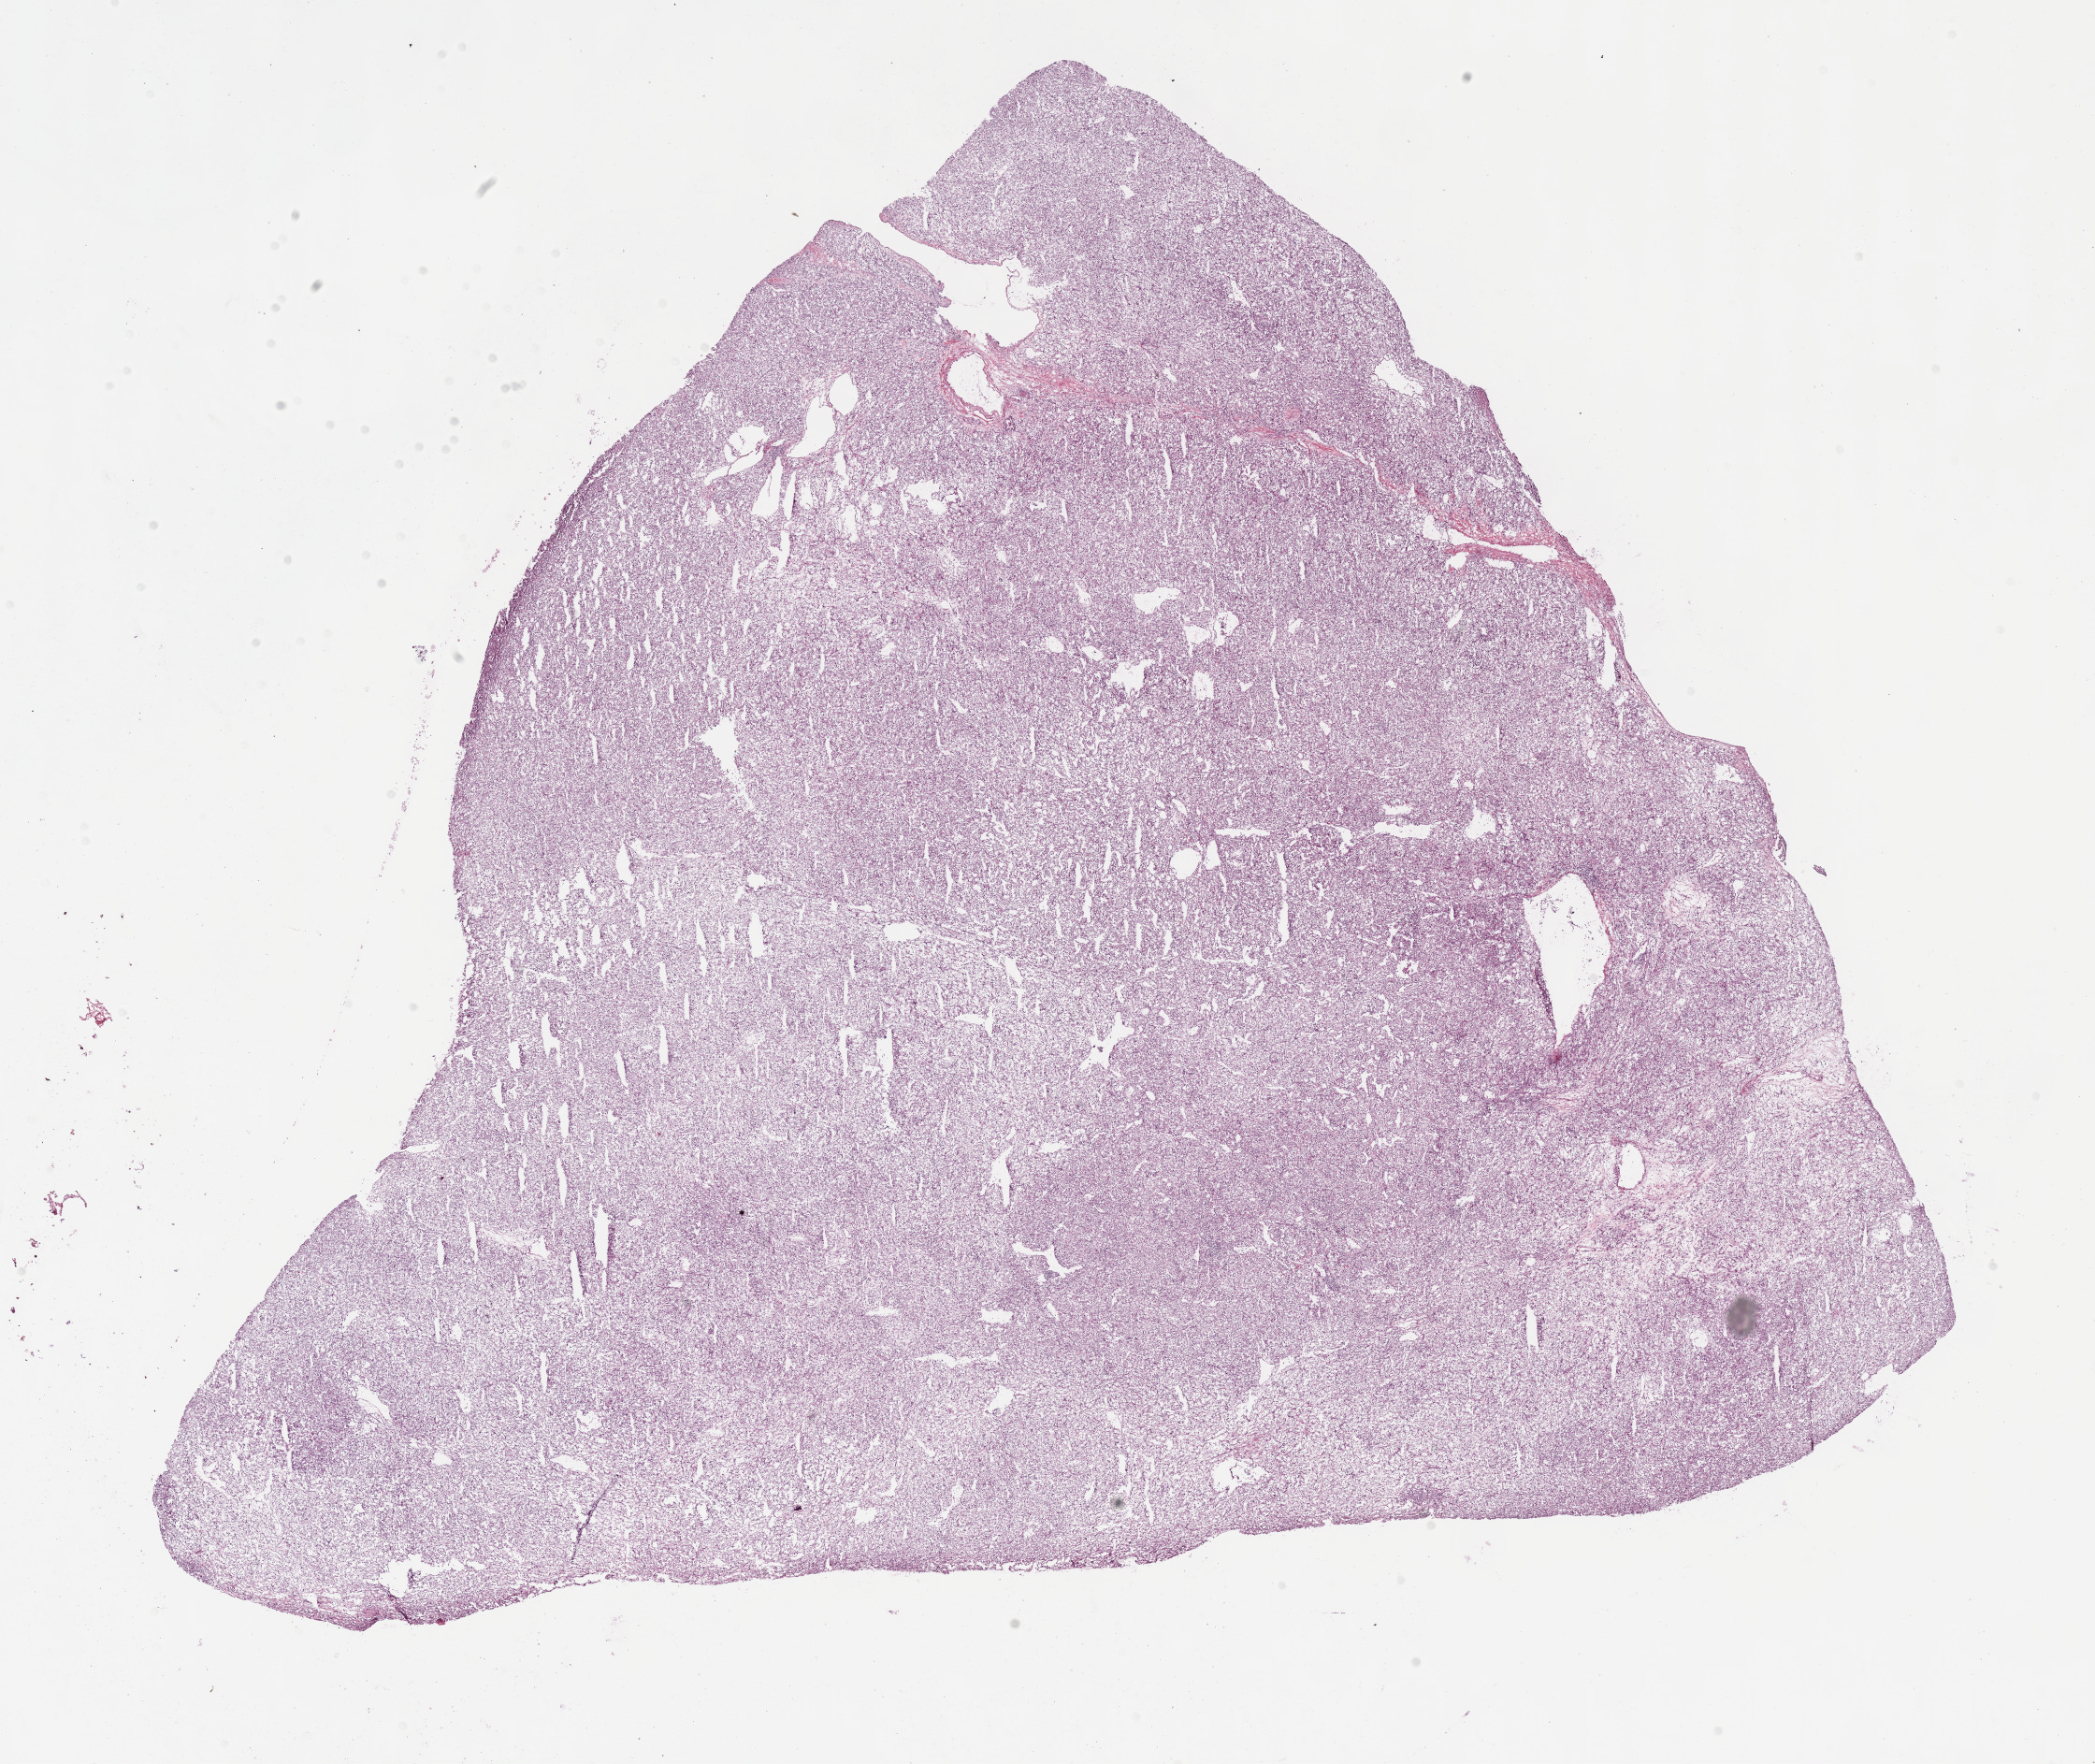
H&E whole-slide image, whole scanned area (about 18.1 x 15.3 mm, slide scanned at 40x) shown as a low-resolution overview, frozen section from the bottom of the tissue portion, primary tumour sample from the kidney. Patient: male, age at initial diagnosis 81 years. Histologic grade: G3 (poorly differentiated). Composition of this section per pathologist review: tumour cells 95%, tumour nuclei 85%, normal cells 0%, stromal cells 5%, necrosis 0%.
• diagnosis: Clear cell adenocarcinoma, NOS
• laterality: right
• AJCC pathologic stage: IV
• lymph nodes positive (case pathology): 0 of 1 examined